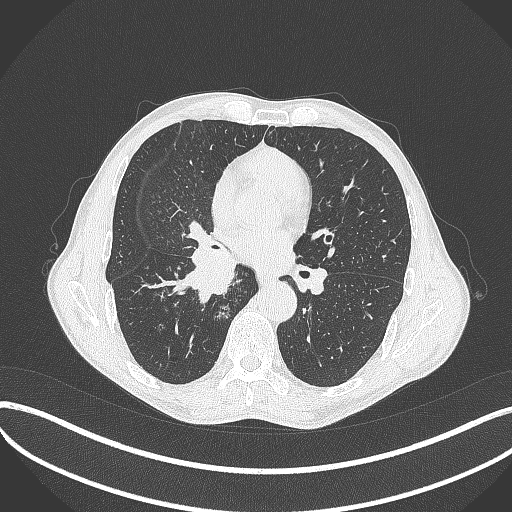
Chest CT, one axial slice; slice 219 of 481 in the series (ordered by position); reconstruction kernel B70f; 120 kVp; lung window (W 1500 / L -600 HU); 512 × 512 image matrix, field of view 400 × 400 mm. Patient: male, 65 years. From the clinical record (not read from this slice): clinical TNM (as recorded): T2a N0 M0; histopathological grade: G2.
Outlined on this slice (bounding box drawn by a radiologist):
- lung tumour (recorded histology: squamous cell carcinoma): bounding box [x1, y1, x2, y2] px = [174, 246, 247, 303]